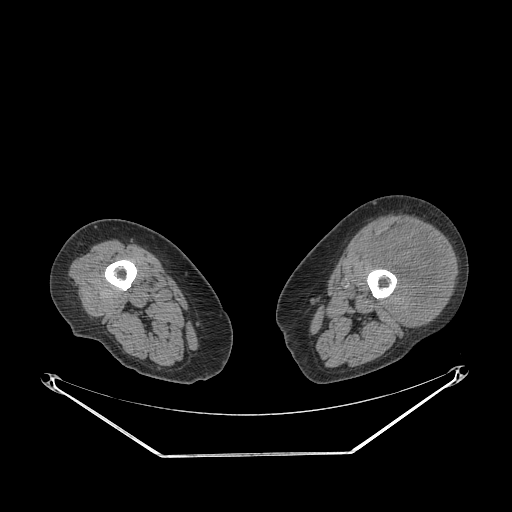
CT of an extremity soft-tissue mass (from a PET/CT study), one axial slice. Position 212 of 267 along the scan axis. Soft-tissue window (W 400 / L 40 HU). 3.75 mm slice thickness. 512 × 512 image matrix, field of view 500 × 500 mm. Female patient. From the clinical record (not read from this slice): histological type: undifferentiated – high grade; grade: high; site of the primary tumour: left thigh.
Structures marked on this image (expert contour drawn on MRI and transferred to this co-registered scan by the dataset authors):
- gross tumour volume including surrounding oedema: bounding box (x1, y1, x2, y2) in pixels: (363, 226, 449, 325)
- gross tumour volume (mass): (372, 231, 448, 325)